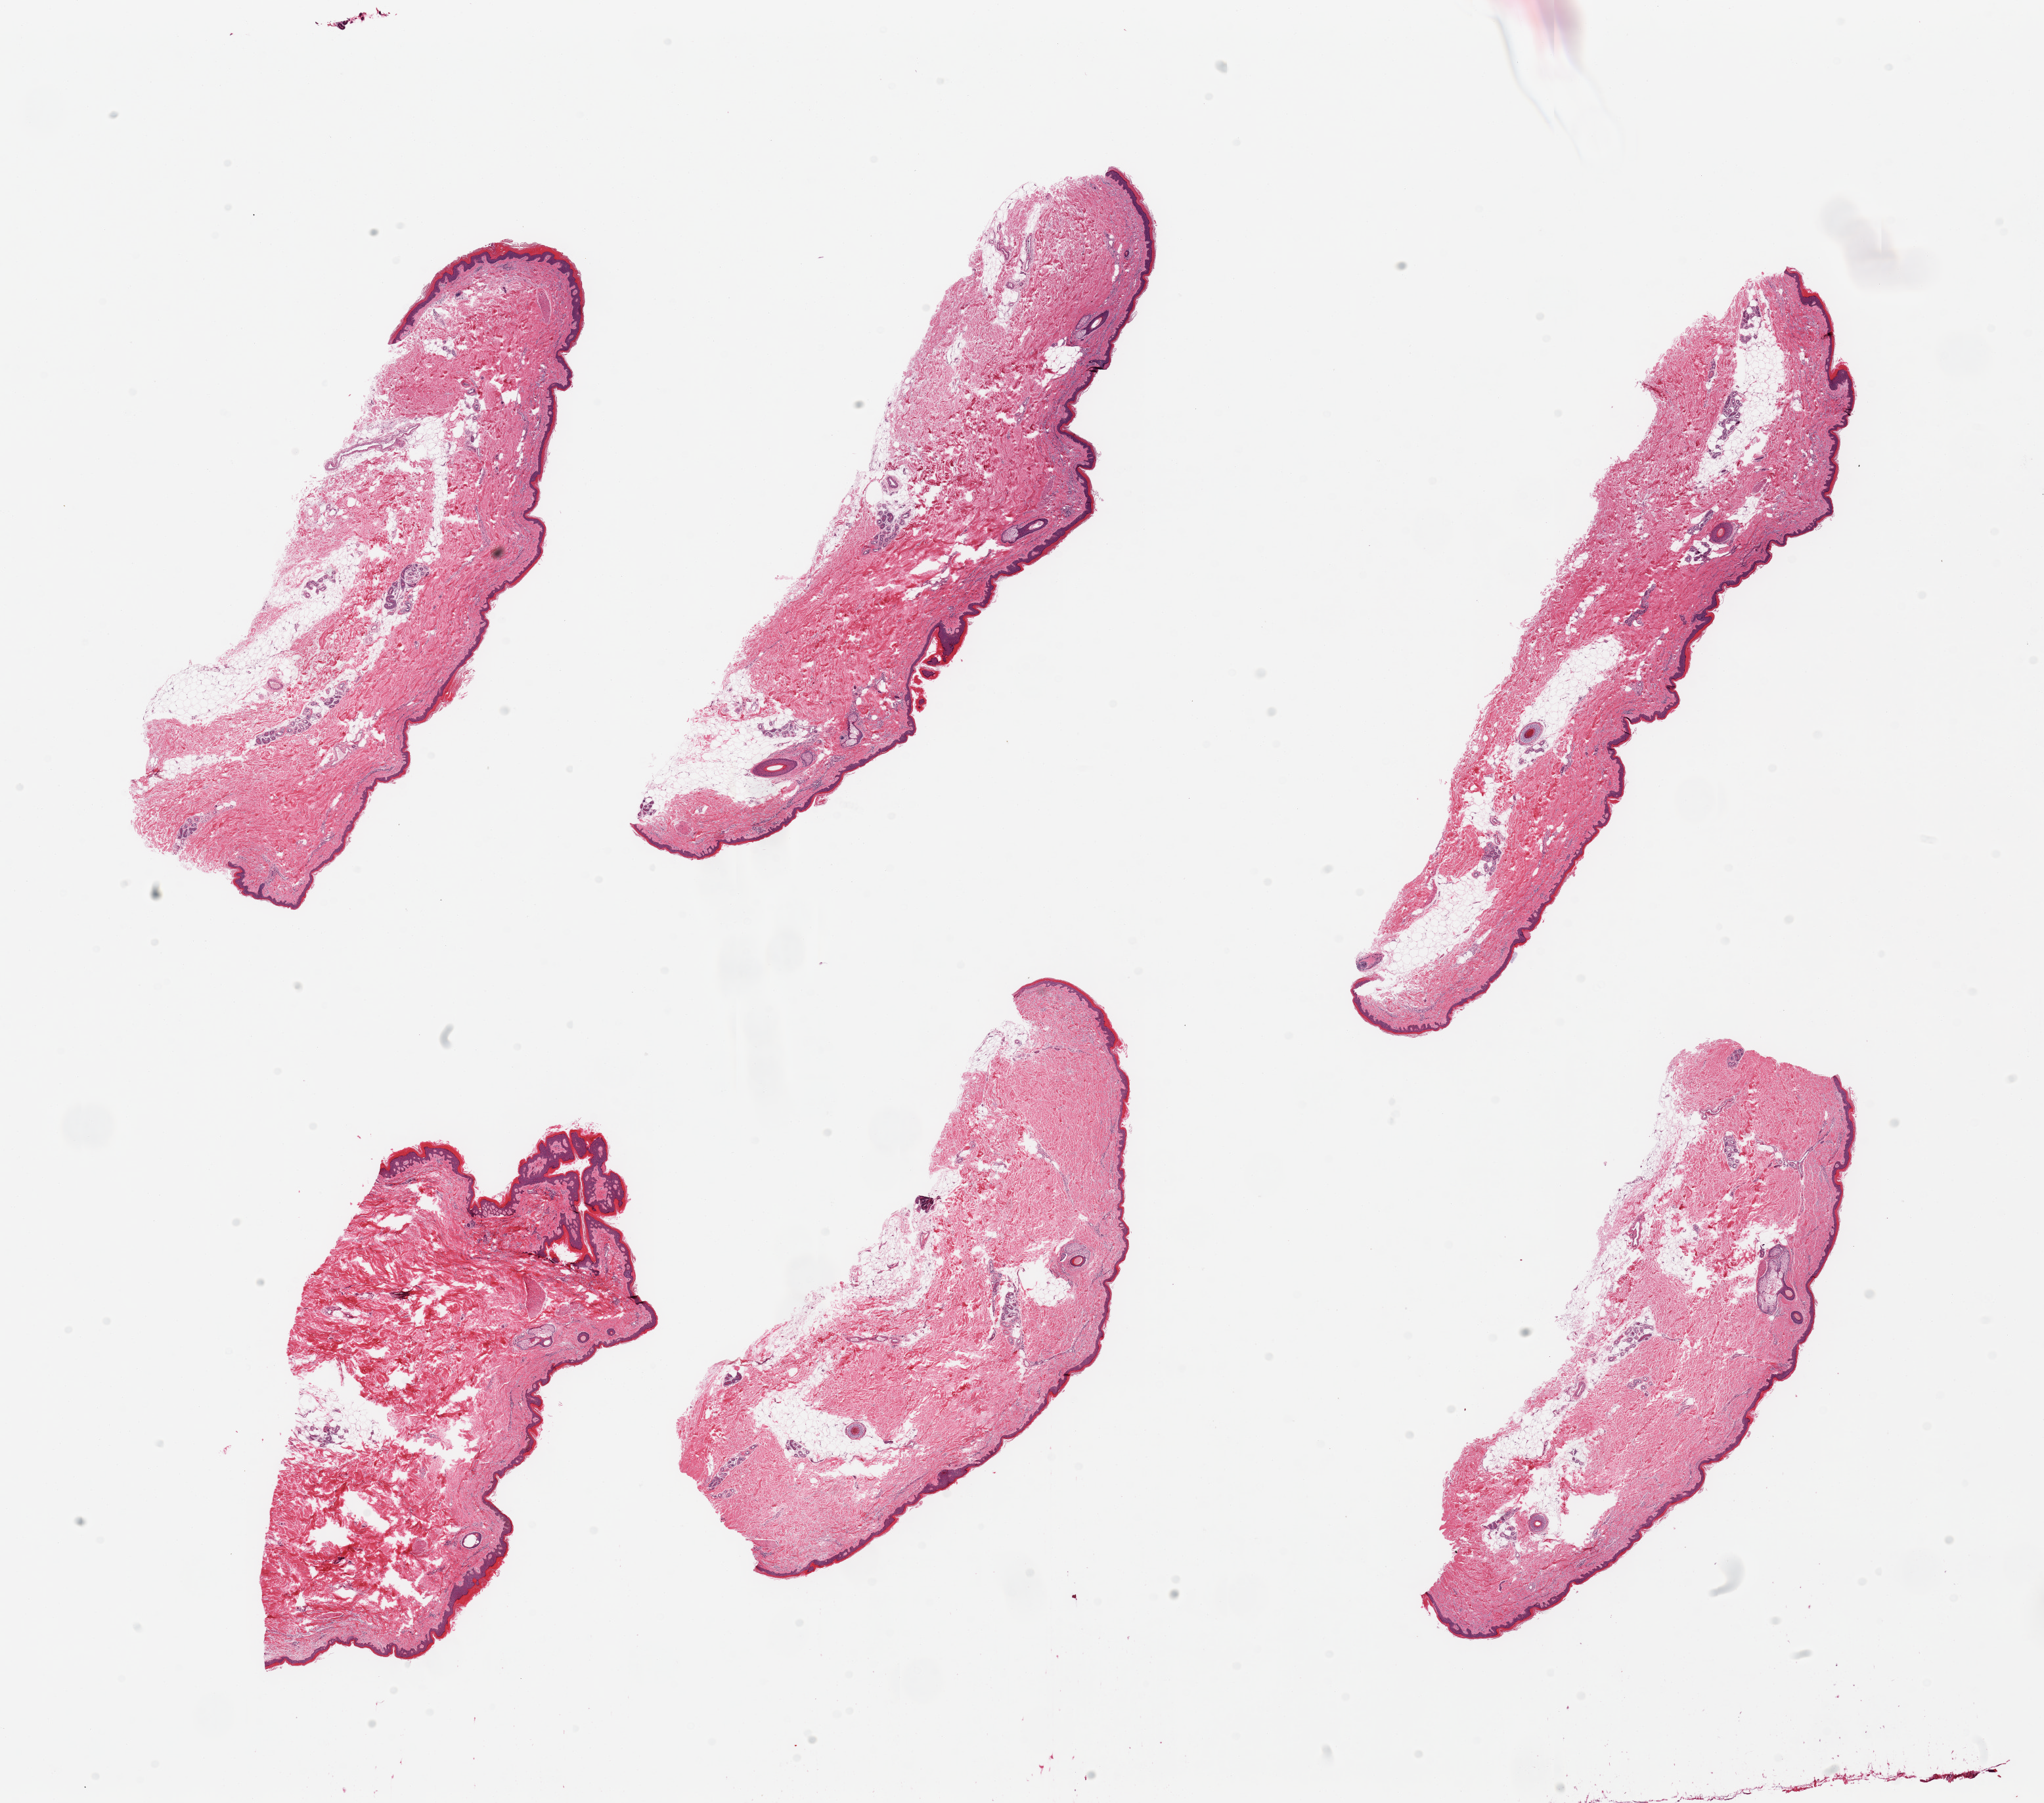
H&E whole-slide image, brightfield — low-resolution overview of the scanned area, about 24.6 x 21.7 mm (acquisition: 20x scan); PAXgene-fixed paraffin-embedded (PFPE) section; target tissue: skin of lower leg; donor tissue sample. Male donor.
Pathologist's review note for this sample: 6 pieces, trace dermal fat; squamous epithelium up to ~4-45 microns.